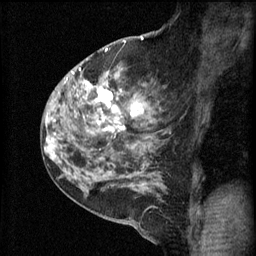
Breast MRI (dynamic contrast-enhanced), one sagittal slice. Slice 37 of 60 in the series (ordered by position). 3 images stored at this slice position (order not interpretable as contrast timing). 1.5 T. TE 4.2 ms, TR 11 ms. 2.3 mm slice thickness. 256 × 256 image matrix, field of view 180 × 180 mm. Patient: female, 52 years.
Outlined on this slice (semi-automatic segmentation, software-assisted and operator-edited):
- analysis volume of interest (the breast-tissue region the enhancement analysis was run in; not a lesion): bounding box <86,76,162,157> (left, top, right, bottom; pixels)
- tumour enhancement mask (voxels above the 70 % enhancement threshold inside the analysis volume of interest): <87,82,144,133>